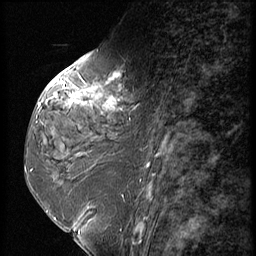
Breast MRI (dynamic contrast-enhanced), one sagittal slice; dynamic contrast-enhanced series, image 2 of 3 at this slice position (ordered by acquisition); 1.5 T; TE 4.2 ms, TR 9 ms; 256 × 256 image matrix. Patient: female, 59 years. Case-level facts recorded for this patient, not image findings: setting: breast cancer imaged before/during neoadjuvant chemotherapy; receptor status: HER2-positive.
Structures marked on this image (semi-automatic segmentation, software-assisted and operator-edited):
- analysis volume of interest (the breast-tissue region the enhancement analysis was run in; not a lesion): bounding box [x1, y1, x2, y2] px = [44, 66, 151, 135]
- tumour enhancement mask (voxels above the 140 % enhancement threshold inside the analysis volume of interest): [52, 75, 120, 108]